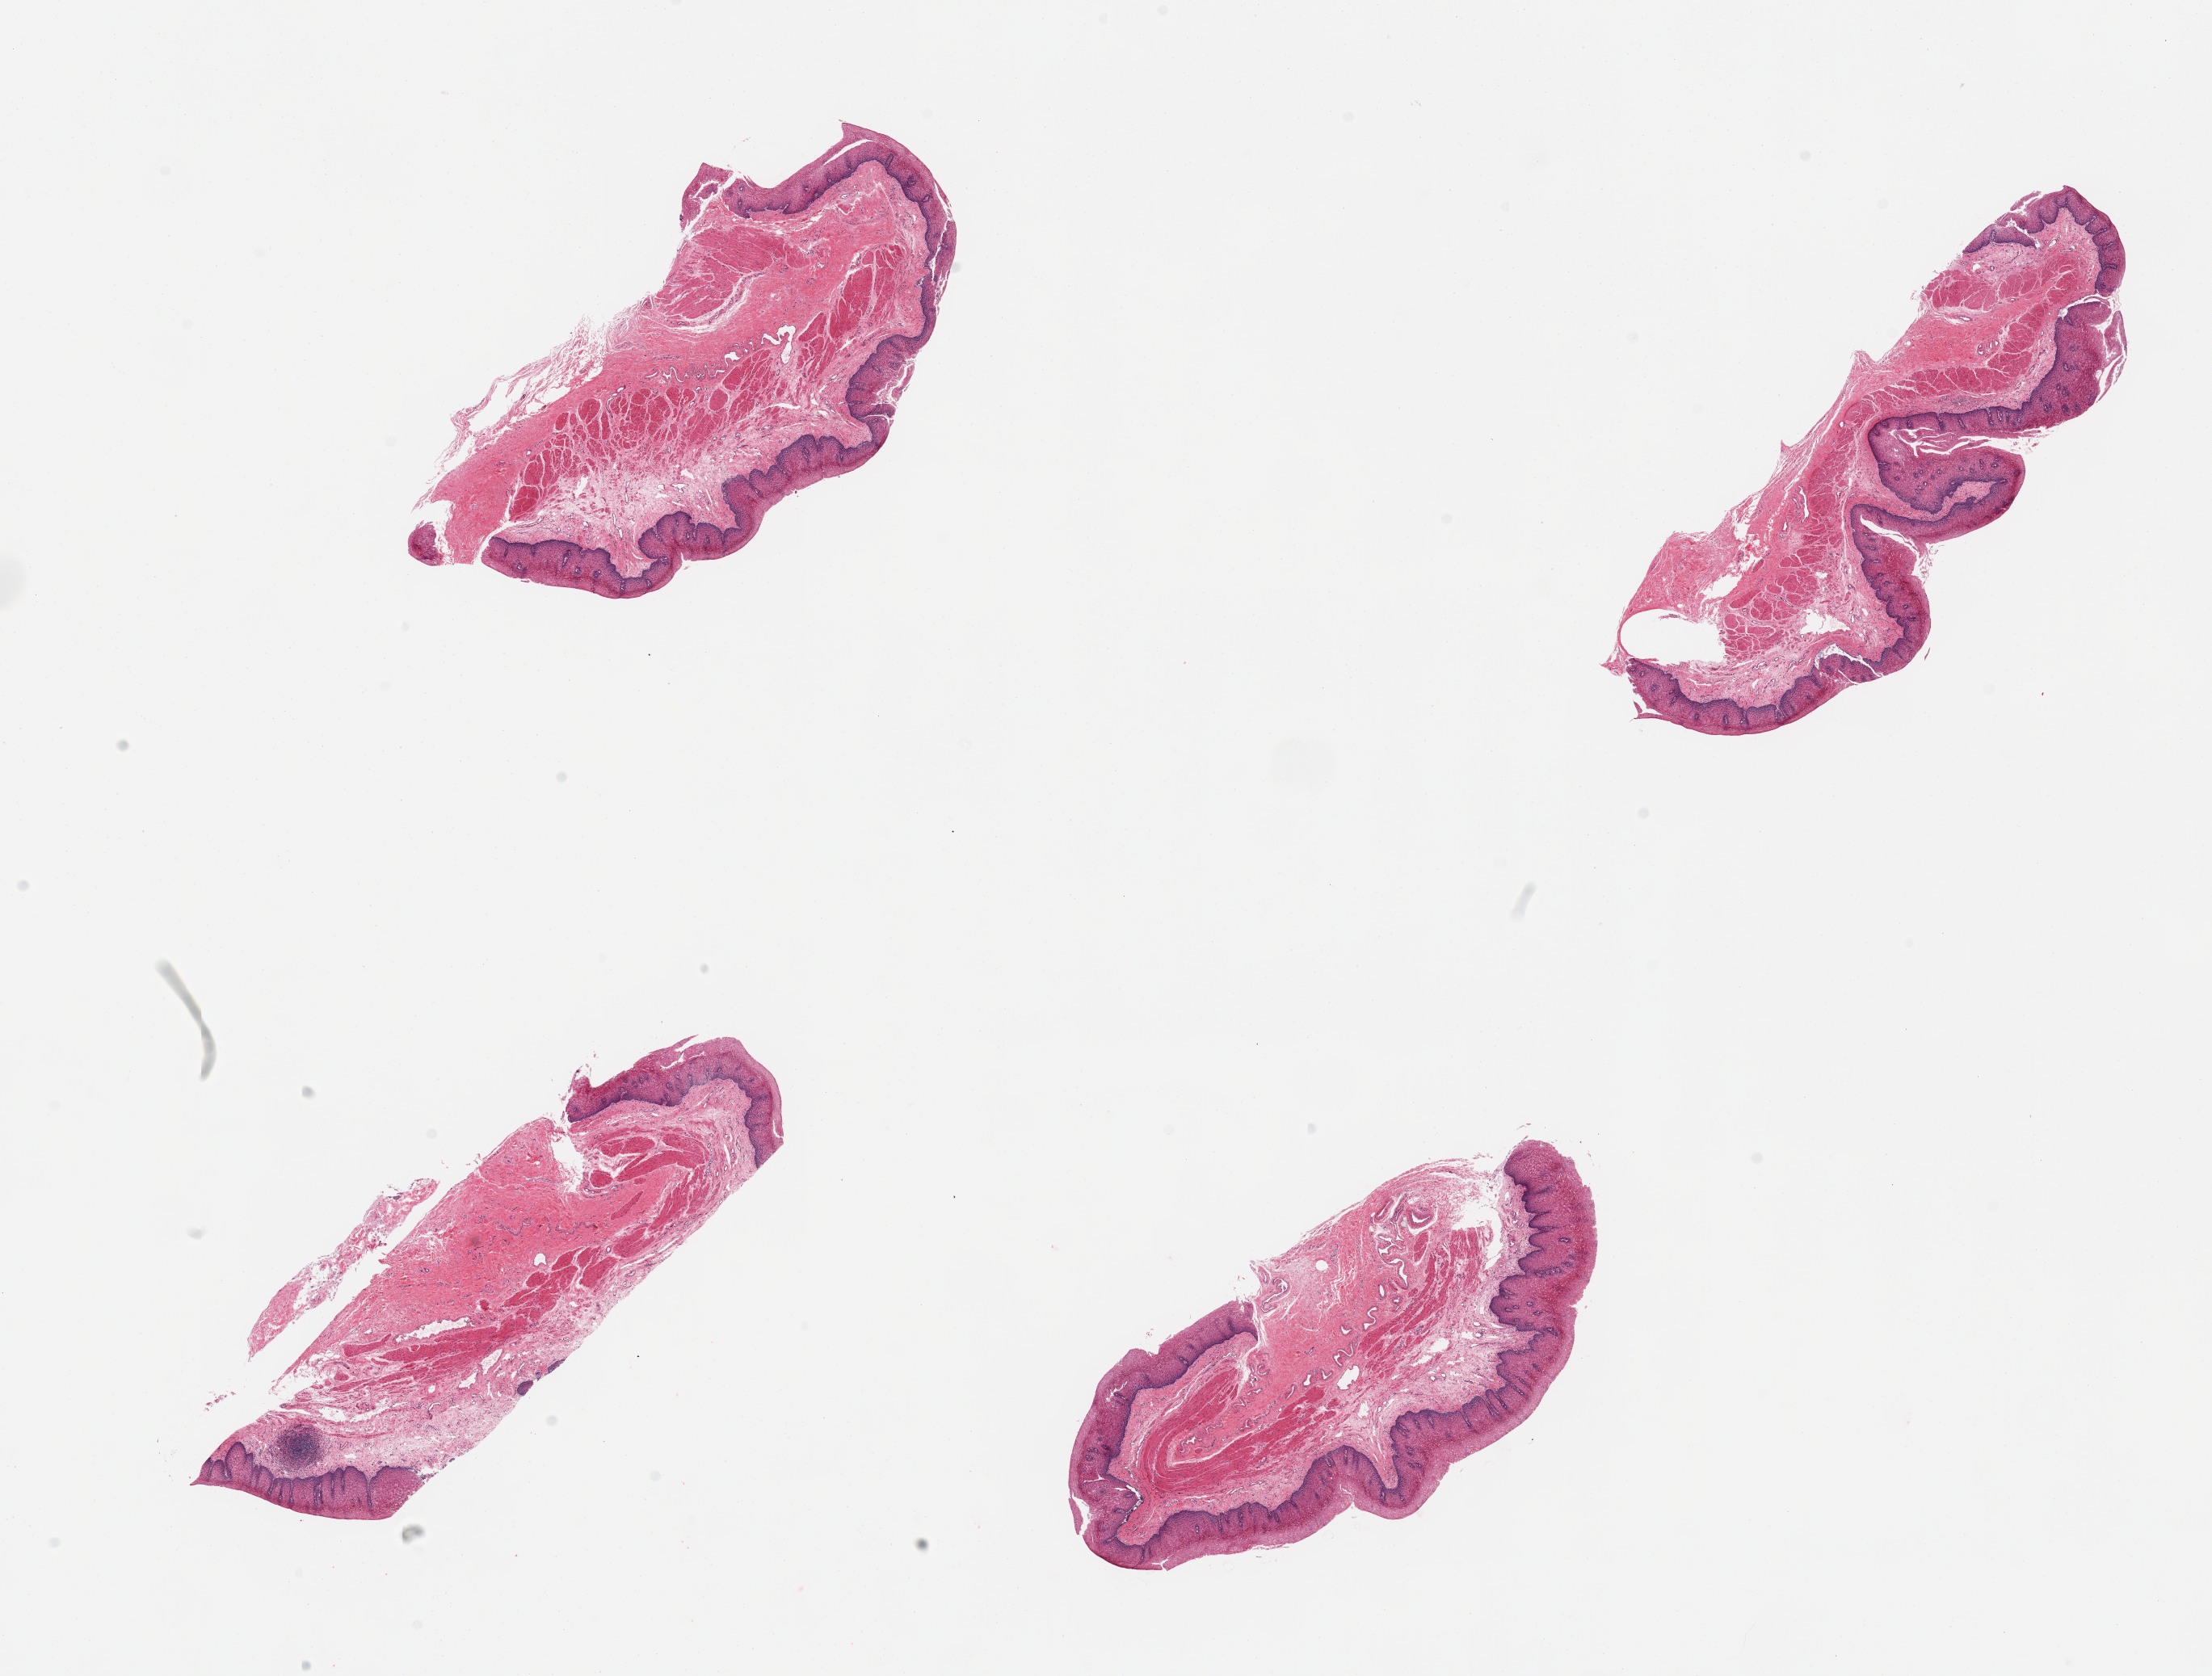
Whole-slide image, H&E stain, whole scanned area (about 21.7 x 16.4 mm) shown as a low-resolution overview. PAXgene-fixed paraffin-embedded (PFPE) section. Target tissue: esophageal mucous membrane. Donor tissue sample. Donor: female.
- review note (as recorded): 4 pieces